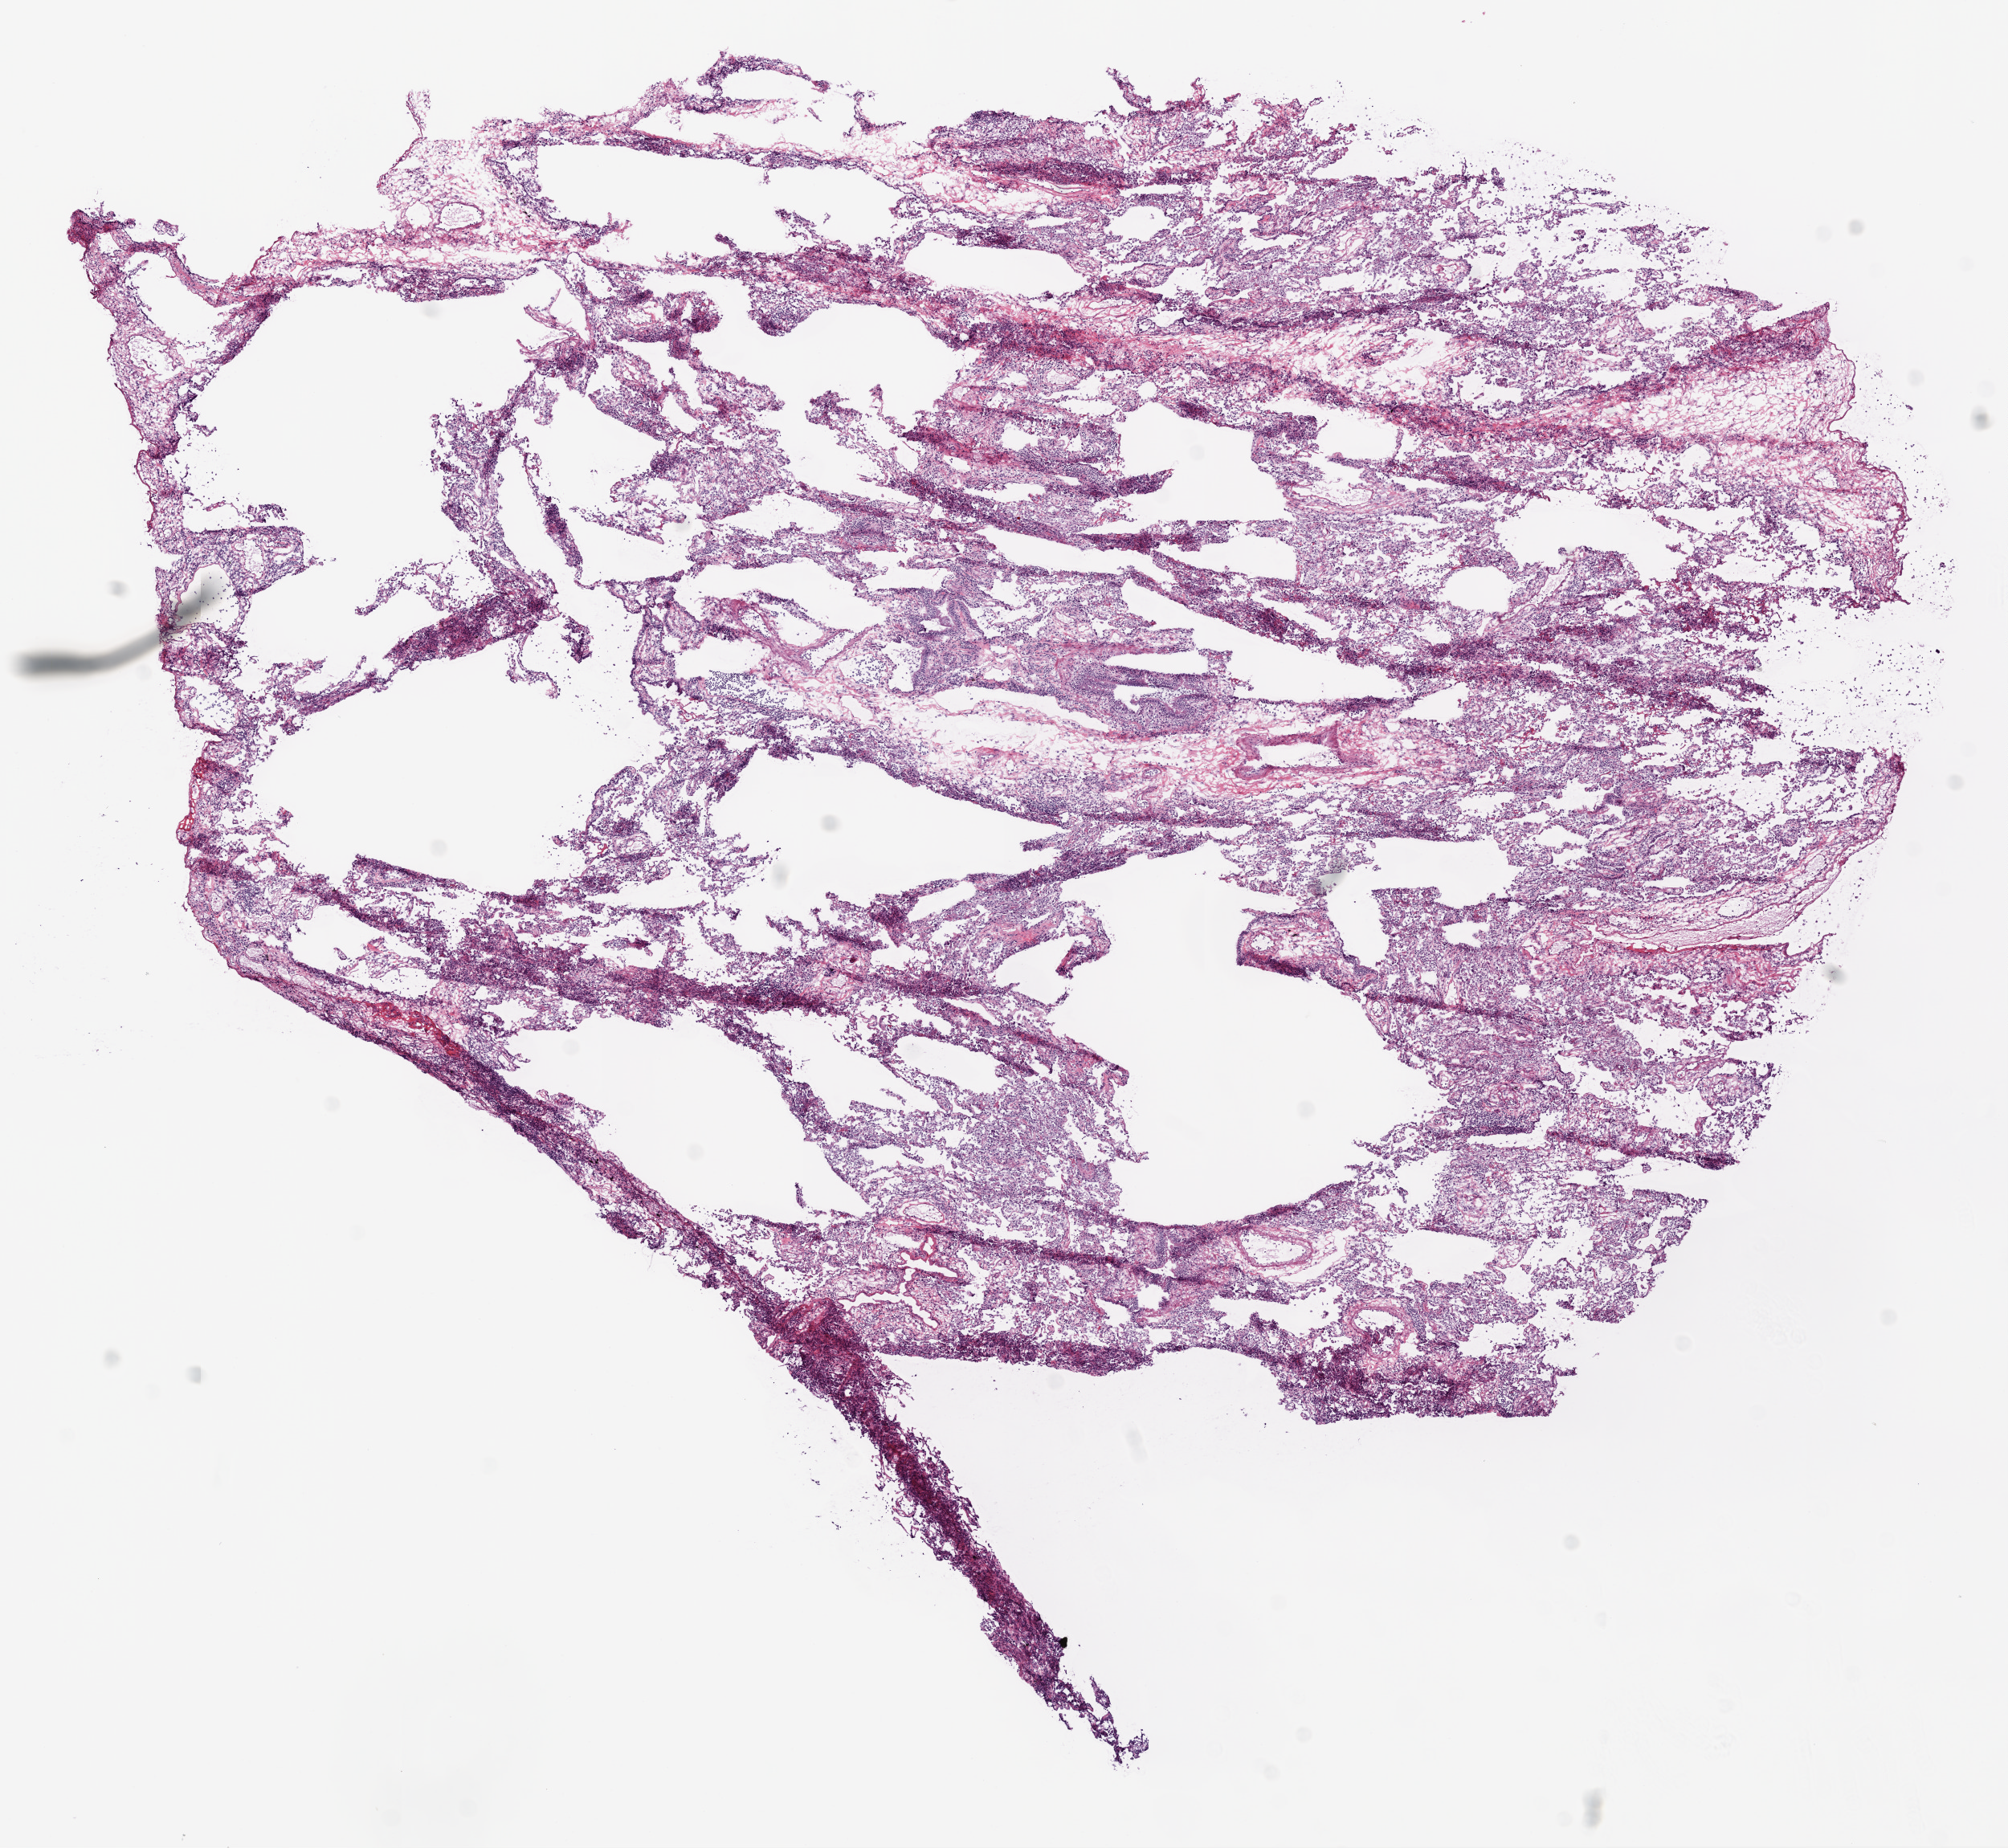
Digitized H&E tissue section (whole slide) — shown as a low-resolution overview of the whole scanned area (about 10.0 x 9.2 mm, acquisition: 20x scan). Frozen section from the bottom of the tissue portion. Solid tissue normal (non-tumour tissue) sample from the lung. Male, age 71 years at initial diagnosis.
- this section: solid tissue normal (non-tumour) sample from the same patient
- patient diagnosis: Squamous cell carcinoma, NOS (upper lobe, lung)